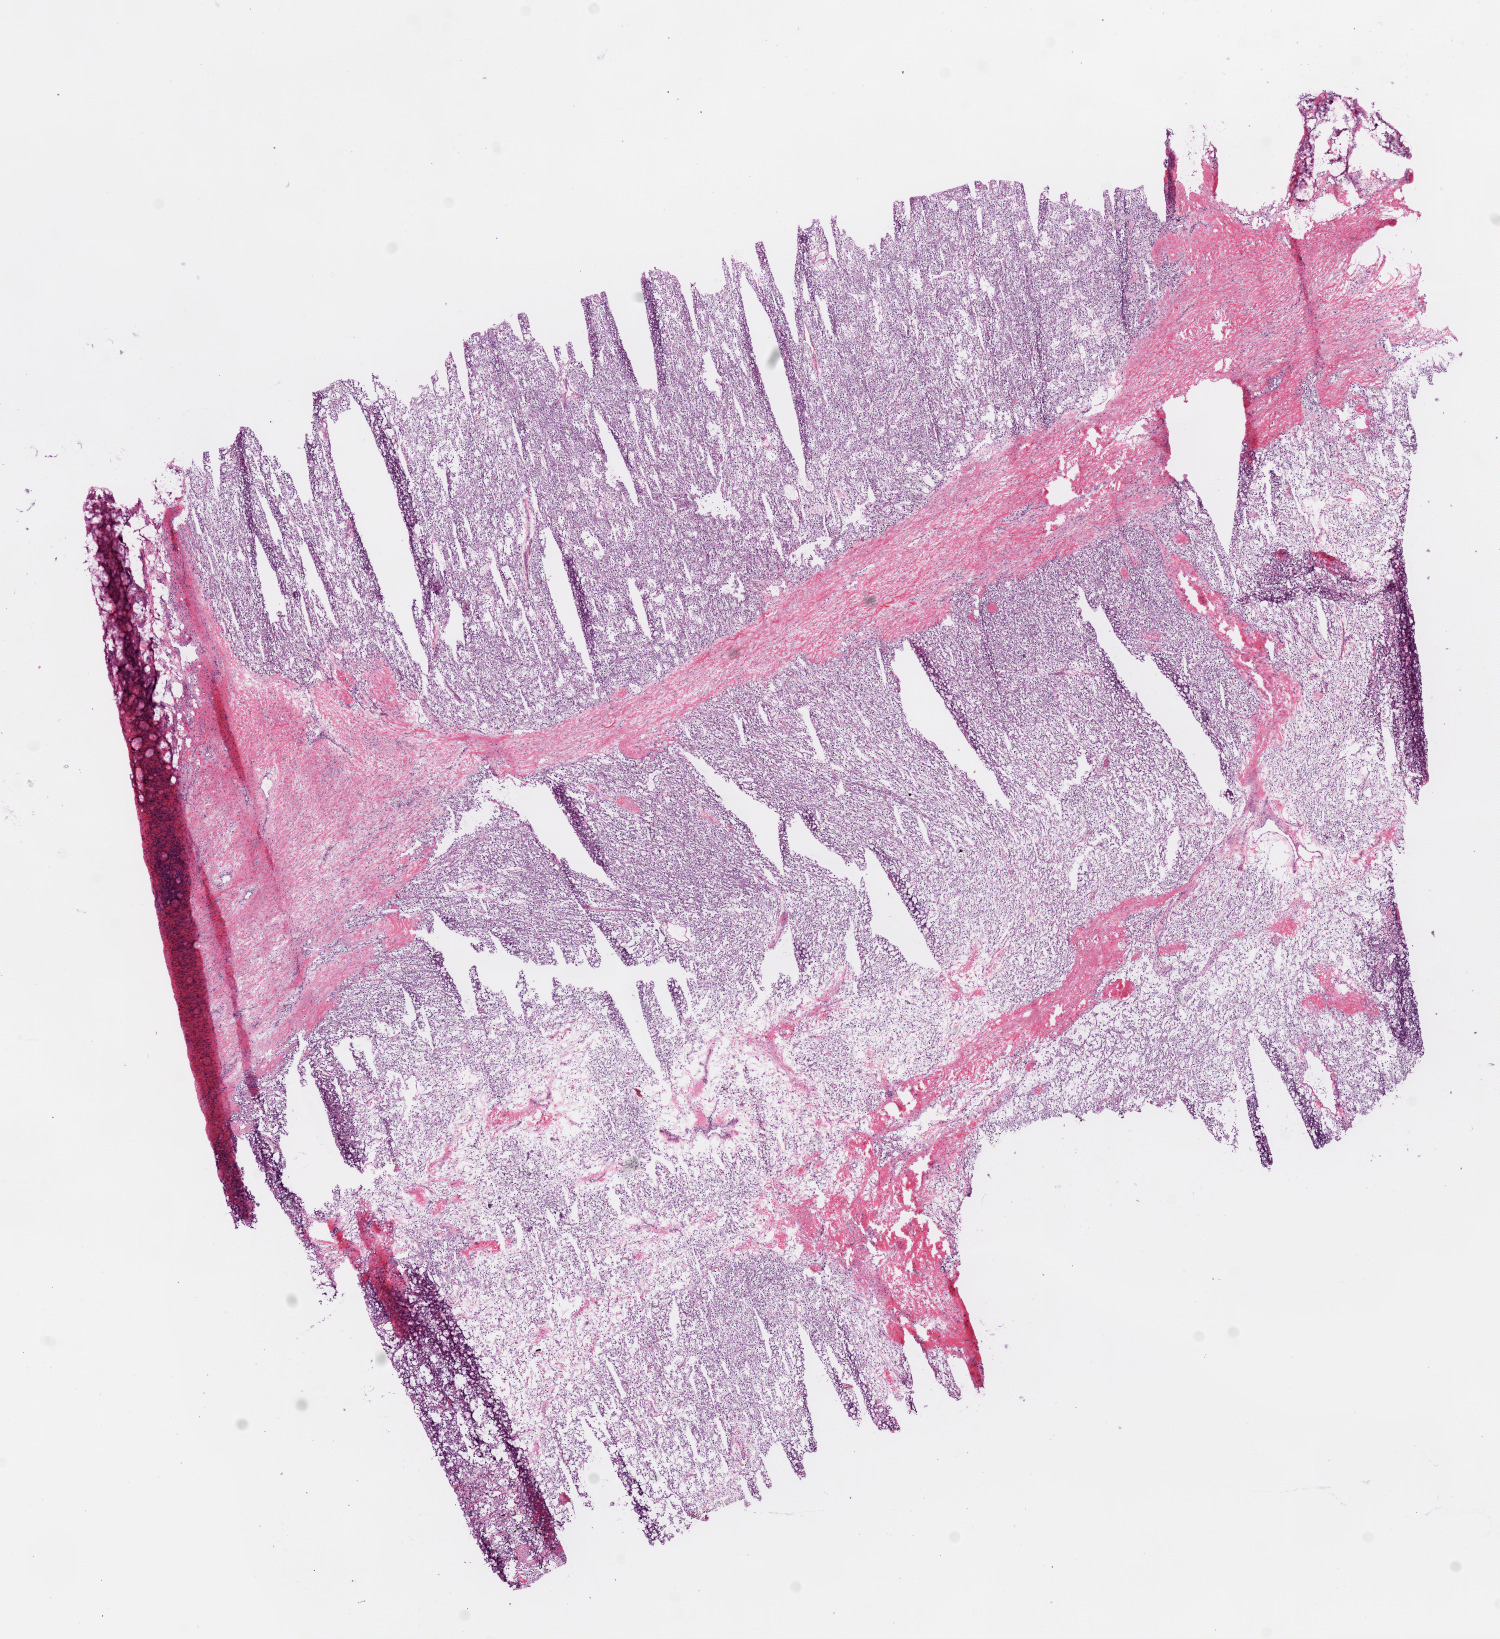
Hematoxylin and eosin (H&E) stained whole-slide image — a low-resolution overview of the entire scanned area, about 12.0 x 13.2 mm (from a 20x scan). Frozen section from the top of the tissue portion. Primary tumour sample from the kidney. Male patient; age at initial diagnosis 57 years. Histologic grade: G3 (poorly differentiated). Pathologist review of this section (percent, as recorded): tumour cells 85%, tumour nuclei 85%, normal cells 0%, stromal cells 15%, necrosis 0%.
Histologic diagnosis: Clear cell adenocarcinoma, NOS. AJCC pathologic stage: II.